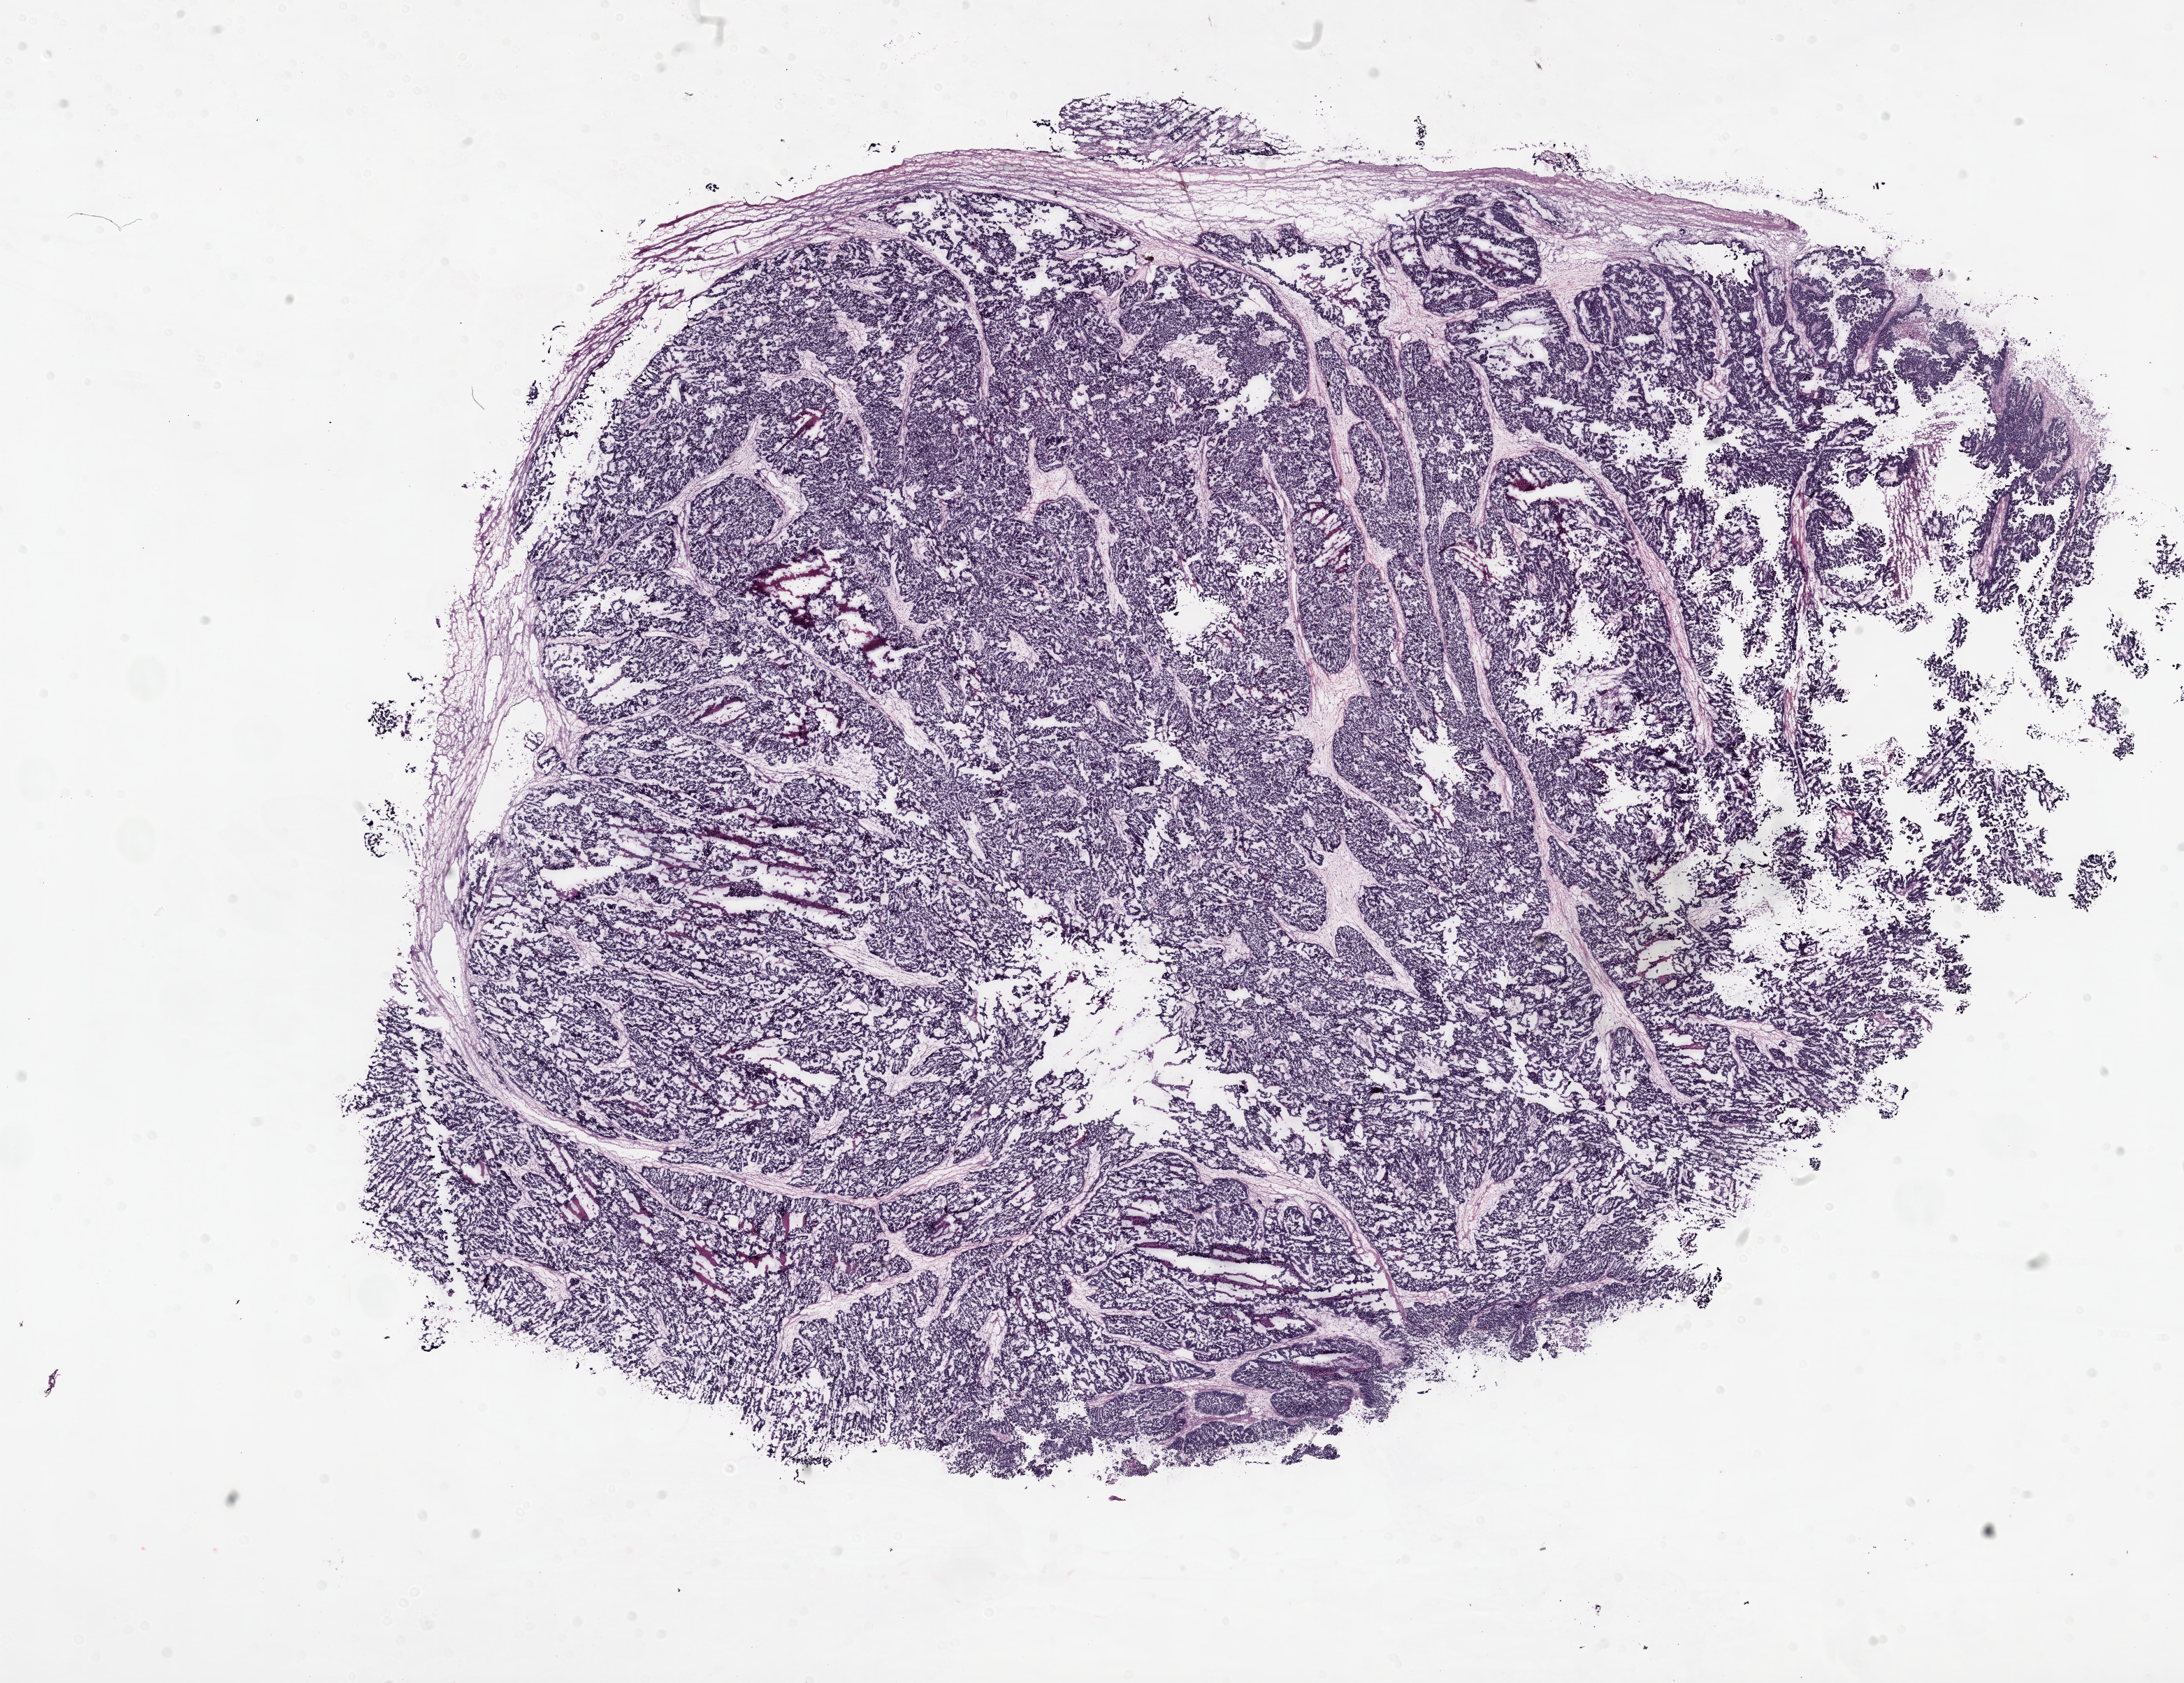
Whole-slide histology image, H&E-stained, a low-resolution overview of the entire scanned area, about 25.1 x 19.3 mm (slide scanned at 20x), frozen section from the top of the tissue portion, primary tumour sample from the ovary. Patient: female, age at initial diagnosis 49 years. Histologic grade: G3 (poorly differentiated). Slide review estimates, as recorded: tumour cells 90%, tumour nuclei 90%, normal cells 0%, stromal cells 5%, necrosis 5%. Infiltration values recorded for this section: lymphocyte infiltration 5%, monocyte infiltration 0%, neutrophil infiltration 0%.
Laterality: bilateral. Pathologic diagnosis: Serous cystadenocarcinoma, NOS. FIGO stage: IV.